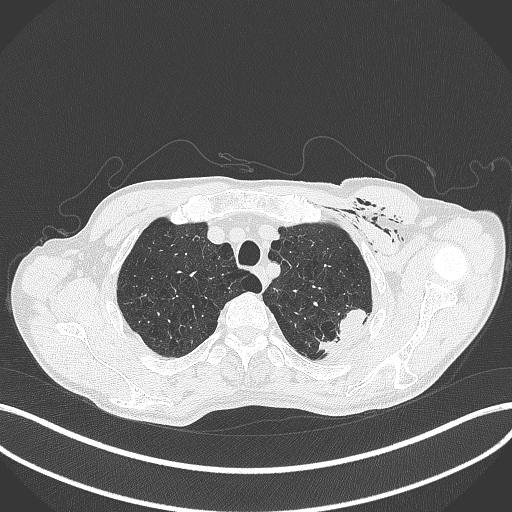
Chest CT, one axial slice. Position 352 of 457 along the scan axis. 120 kVp. Lung window (W 1500 / L -600 HU). 1 mm slice thickness. 512 × 512 image matrix, field of view 400 × 400 mm. Patient: male, 58 years. Case-level facts recorded for this patient, not image findings: clinical TNM (as recorded): T3 N0 M0.
Annotated regions visible in this slice (bounding box drawn by a radiologist):
- lung tumour (recorded histology: adenocarcinoma): bounding box (x1, y1, x2, y2) in pixels: (307, 305, 371, 356)